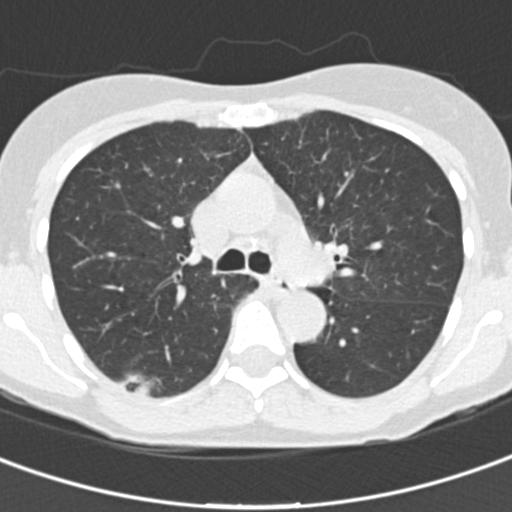
Low-dose screening chest CT, axial slice; first (baseline) screen; lung window (W 1500 / L -600 HU); 2 mm slice thickness; standard (soft-tissue) reconstruction kernel (B30f). Female participant, aged 64 years at enrolment. Current smoker at enrolment.
Expert reader's lesion annotation, box from (x=86, y=349) to (x=179, y=419) px. Screening reader's record for this exam (one nodule recorded; not confirmed to be the boxed lesion): non-calcified nodule or mass ≥4 mm, right lower lobe, 31 × 15 mm, poorly defined margins, ground glass attenuation.